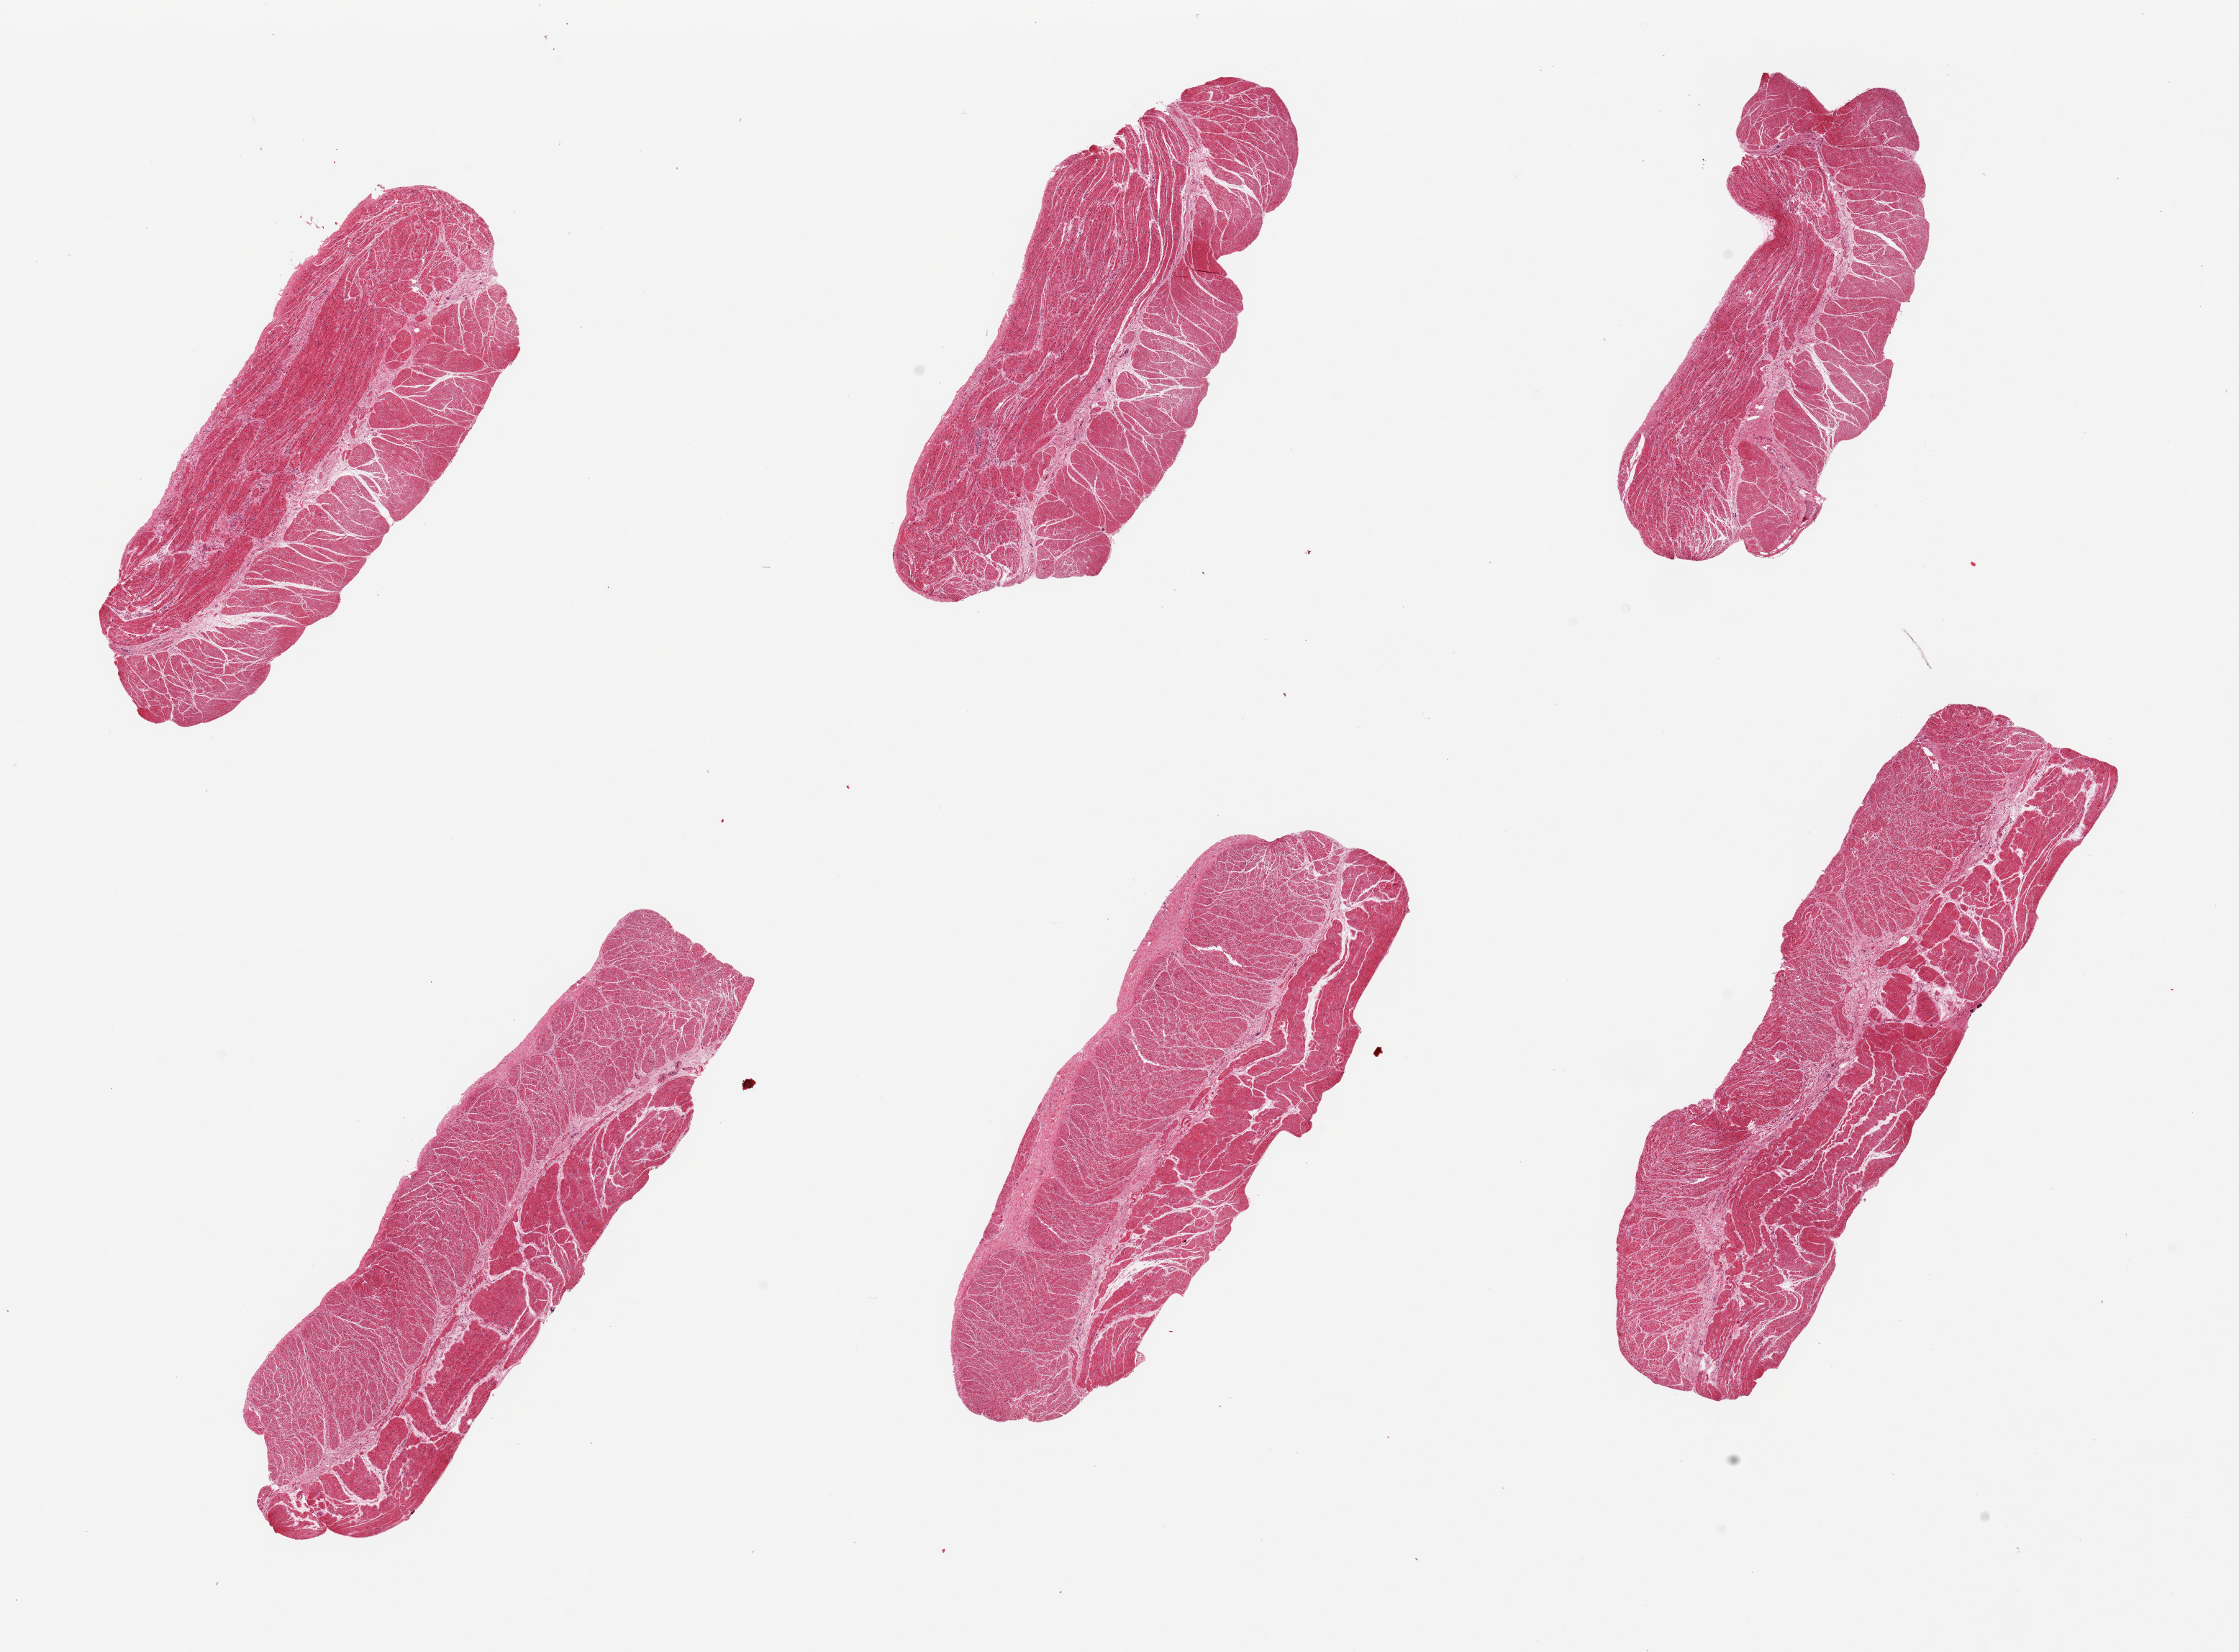
Hematoxylin and eosin (H&E) whole-slide image — shown as a low-resolution overview of the whole scanned area (about 24.6 x 18.2 mm, slide scanned at 20x); PAXgene-fixed paraffin-embedded (PFPE) section; sampled site (target tissue): gastroesophageal junction; tissue donor sample. Donor: male.
- pathologist's review note for this sample: 6 pieces, all muscularis